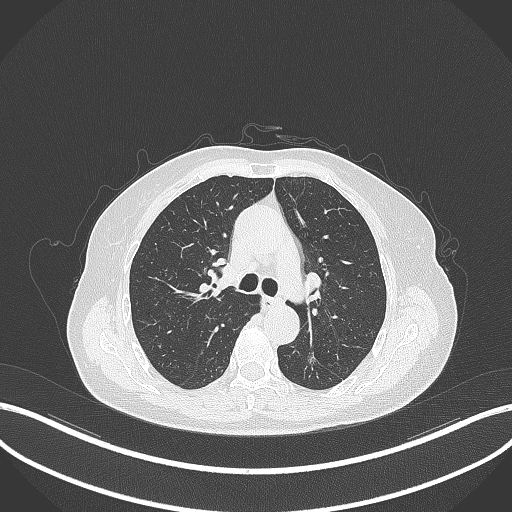
Chest CT, one axial slice. Position 199 of 352 along the scan axis. Lung window (W 1500 / L -600 HU). 512 × 512 image matrix, field of view 400 × 400 mm. Patient: female, 70 years. From the clinical record (not read from this slice): clinical TNM (as recorded): T1c N0 M0.
Structures marked on this image (rectangle marked by the reading radiologist):
- lung tumour (recorded histology: adenocarcinoma): bounding box <301,343,322,373> (left, top, right, bottom; pixels)